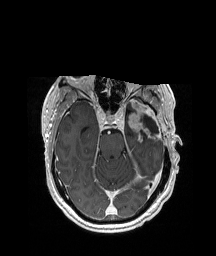
Brain MRI from a brain-tumour surgery series, one axial slice; slice 131 of 208 in the series (ordered by position); T1-weighted post-contrast; 216 × 256 image matrix, field of view 228 × 270 mm. Case-level facts recorded for this patient, not image findings: histopathology: Glioblastoma; WHO grade: 4; IDH mutation: no; tumour location: Left Anterior/Superior Temporal.
Structures marked on this image (expert manual segmentation):
- previous resection cavity: bounding box (x1, y1, x2, y2) in pixels: (140, 114, 159, 134)
- tumour: (124, 99, 150, 144)